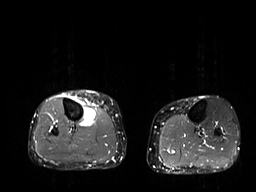
MRI of an extremity soft-tissue mass, one axial slice; position 16 of 32 along the scan axis; STIR; 256 × 192 image matrix, field of view 375 × 281 mm. Female patient. Case-level facts recorded for this patient, not image findings: histological type: undifferentiated – high grade; grade: high; site of the primary tumour: right thigh.
Annotated regions visible in this slice (expert manual segmentation):
- gross tumour volume (mass): bounding box <77,102,97,127> (left, top, right, bottom; pixels)